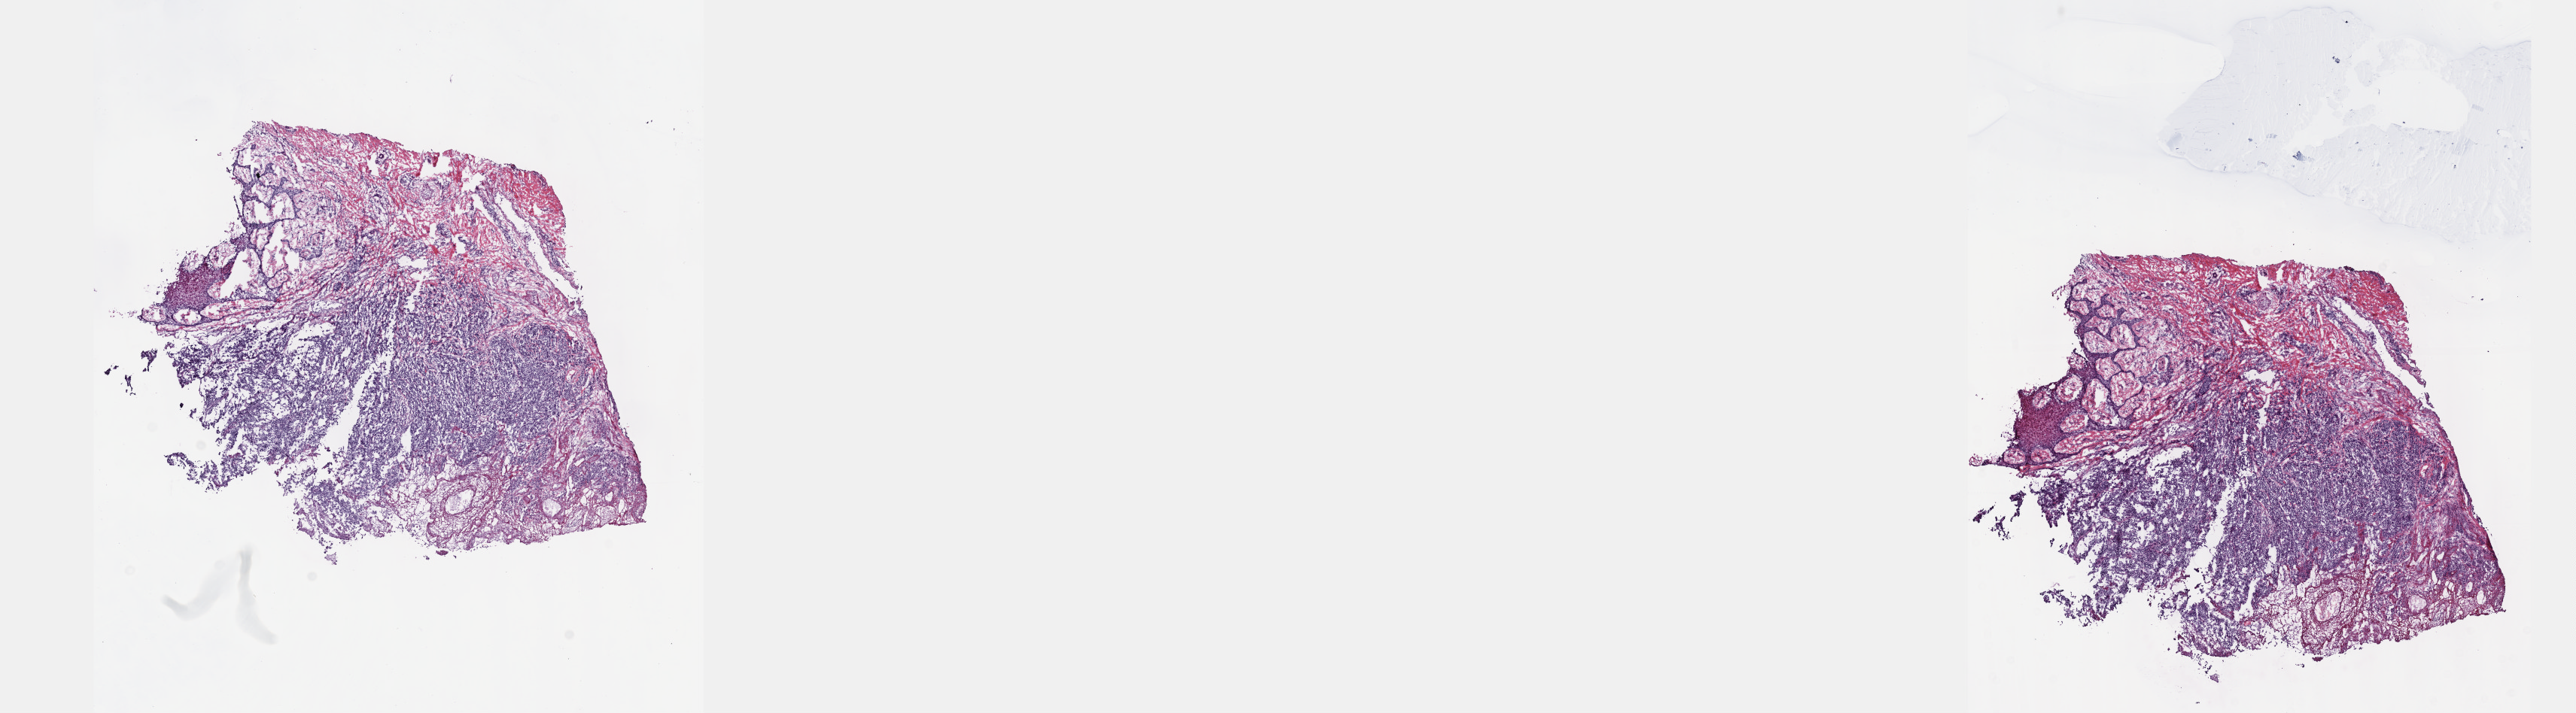
Whole-slide histology image, Hematoxylin and eosin (H&E) stained, low-resolution overview of the scanned area, about 27.7 x 7.7 mm; frozen section; primary tumour sample from the skin. Male, age 81 years at initial diagnosis. Pathologist review of this section (percent, as recorded): tumour cells 50%, tumour nuclei 65%, normal cells 50%, stromal cells 0%, necrosis 0%. Inflammatory infiltration, as recorded: lymphocyte infiltration 0%, monocyte infiltration 0%, neutrophil infiltration 0%.
• pathologic diagnosis: Malignant melanoma, NOS
• AJCC pathologic stage: I (7th edition)